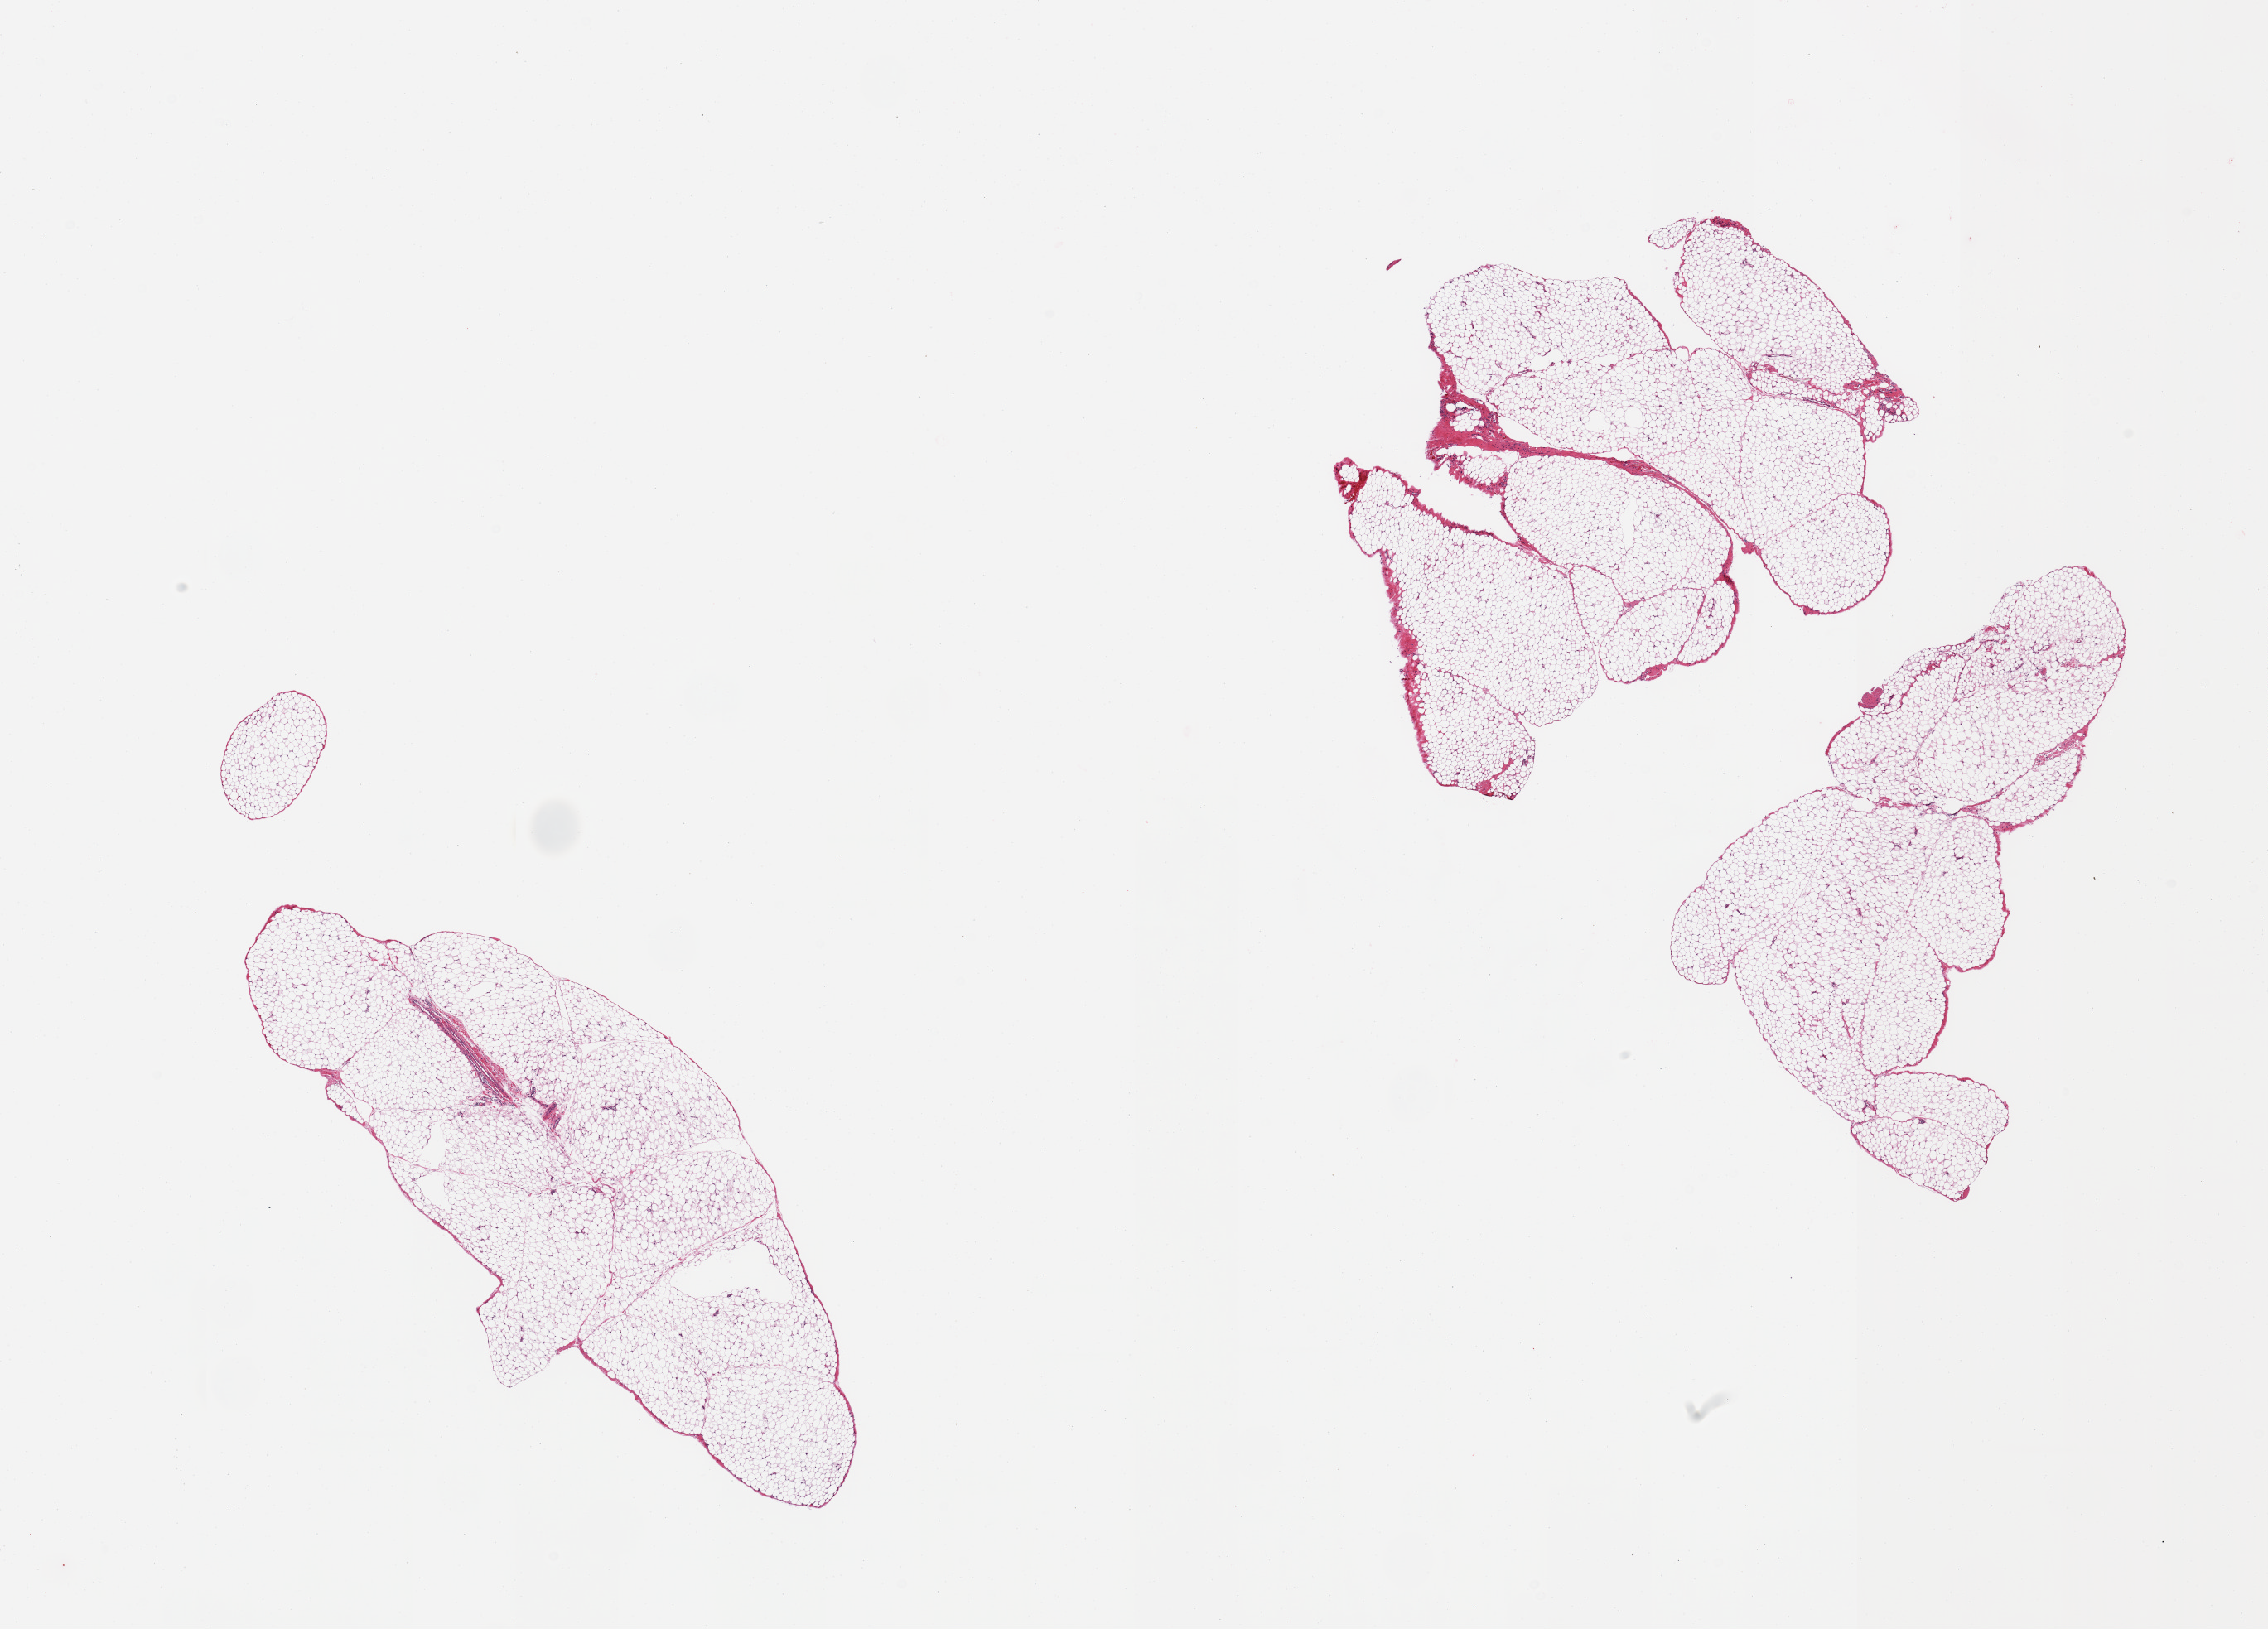
H&E whole-slide image, whole scanned area (about 21.7 x 15.6 mm) shown as a low-resolution overview, PAXgene-fixed paraffin-embedded (PFPE) section, target tissue: omentum, tissue donor sample. Female donor.
Reviewer comment on this tissue sample: 2 pieces; lobulated mature adipose tissue with.